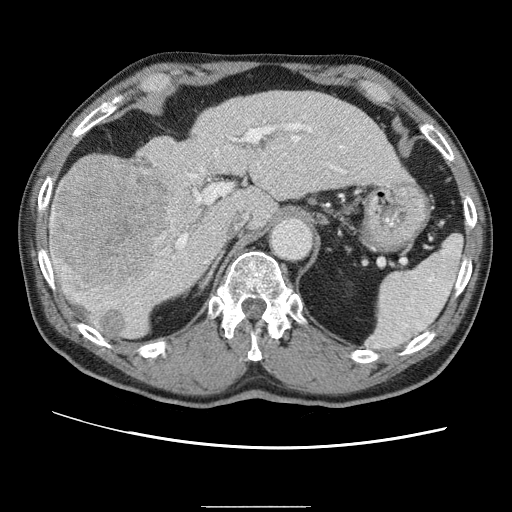
Contrast-enhanced abdominal CT (liver protocol), one axial slice; slice 36 of 75 in the series (ordered by position); reconstruction kernel STANDARD; one of 2 acquisitions stored at this slice position; soft-tissue window (W 400 / L 40 HU); 2.5 mm slice thickness; 512 × 512 image matrix. Case-level facts recorded for this patient, not image findings: diagnosis: hepatocellular carcinoma (patient treated with transarterial chemoembolisation; whether this scan precedes or follows treatment is not stated here); TNM stage (as recorded): Stage-II; Child-Pugh class: A; tumour size: 2 cm.
Outlined on this slice (semi-automatic segmentation, software-assisted and operator-edited):
- liver parenchyma outside the tumour (the mass and vessels are separate outlines, so this box may not span the whole liver): box from (x=50, y=92) to (x=404, y=338) px
- mass: (x=51, y=161)–(x=169, y=305)
- liver vessels: (x=132, y=125)–(x=365, y=307)